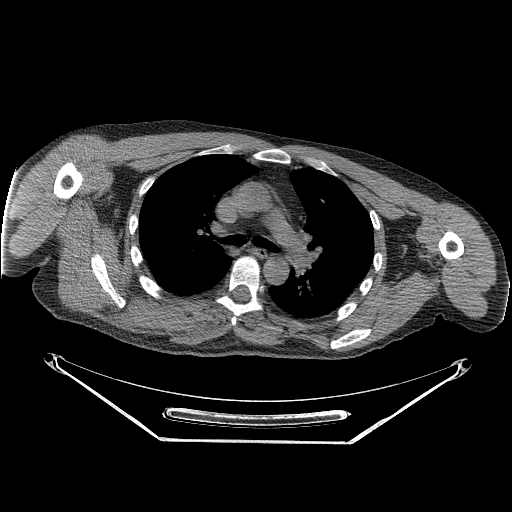
CT of an extremity soft-tissue mass (from a PET/CT study), one axial slice. Position 181 of 267 along the scan axis. Reconstruction kernel STANDARD. 140 kVp. Soft-tissue window (W 400 / L 40 HU). 512 × 512 image matrix, field of view 500 × 500 mm. Male patient. Case-level facts recorded for this patient, not image findings: histological type: pleiomorphic spindle cell undifferentiated; grade: high; site of the primary tumour: right parascapusular.
Structures marked on this image (expert contour drawn on MRI and transferred to this co-registered scan by the dataset authors):
- gross tumour volume including surrounding oedema: bounding box <93,289,218,336> (left, top, right, bottom; pixels)
- gross tumour volume (mass): <119,290,161,327>